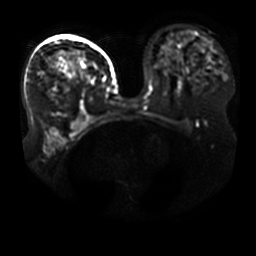
Breast MRI, one axial slice. Position 25 of 41 along the scan axis. Diffusion-weighted series; image 2 of 4 stored at this slice position (different b-values; order by instance number). 3 T. 5 mm slice thickness. 256 × 256 image matrix, field of view 400 × 400 mm. Female patient.
Outlined on this slice (manually delineated by an expert):
- tumour on diffusion-weighted imaging: box from (x=51, y=51) to (x=94, y=85) px